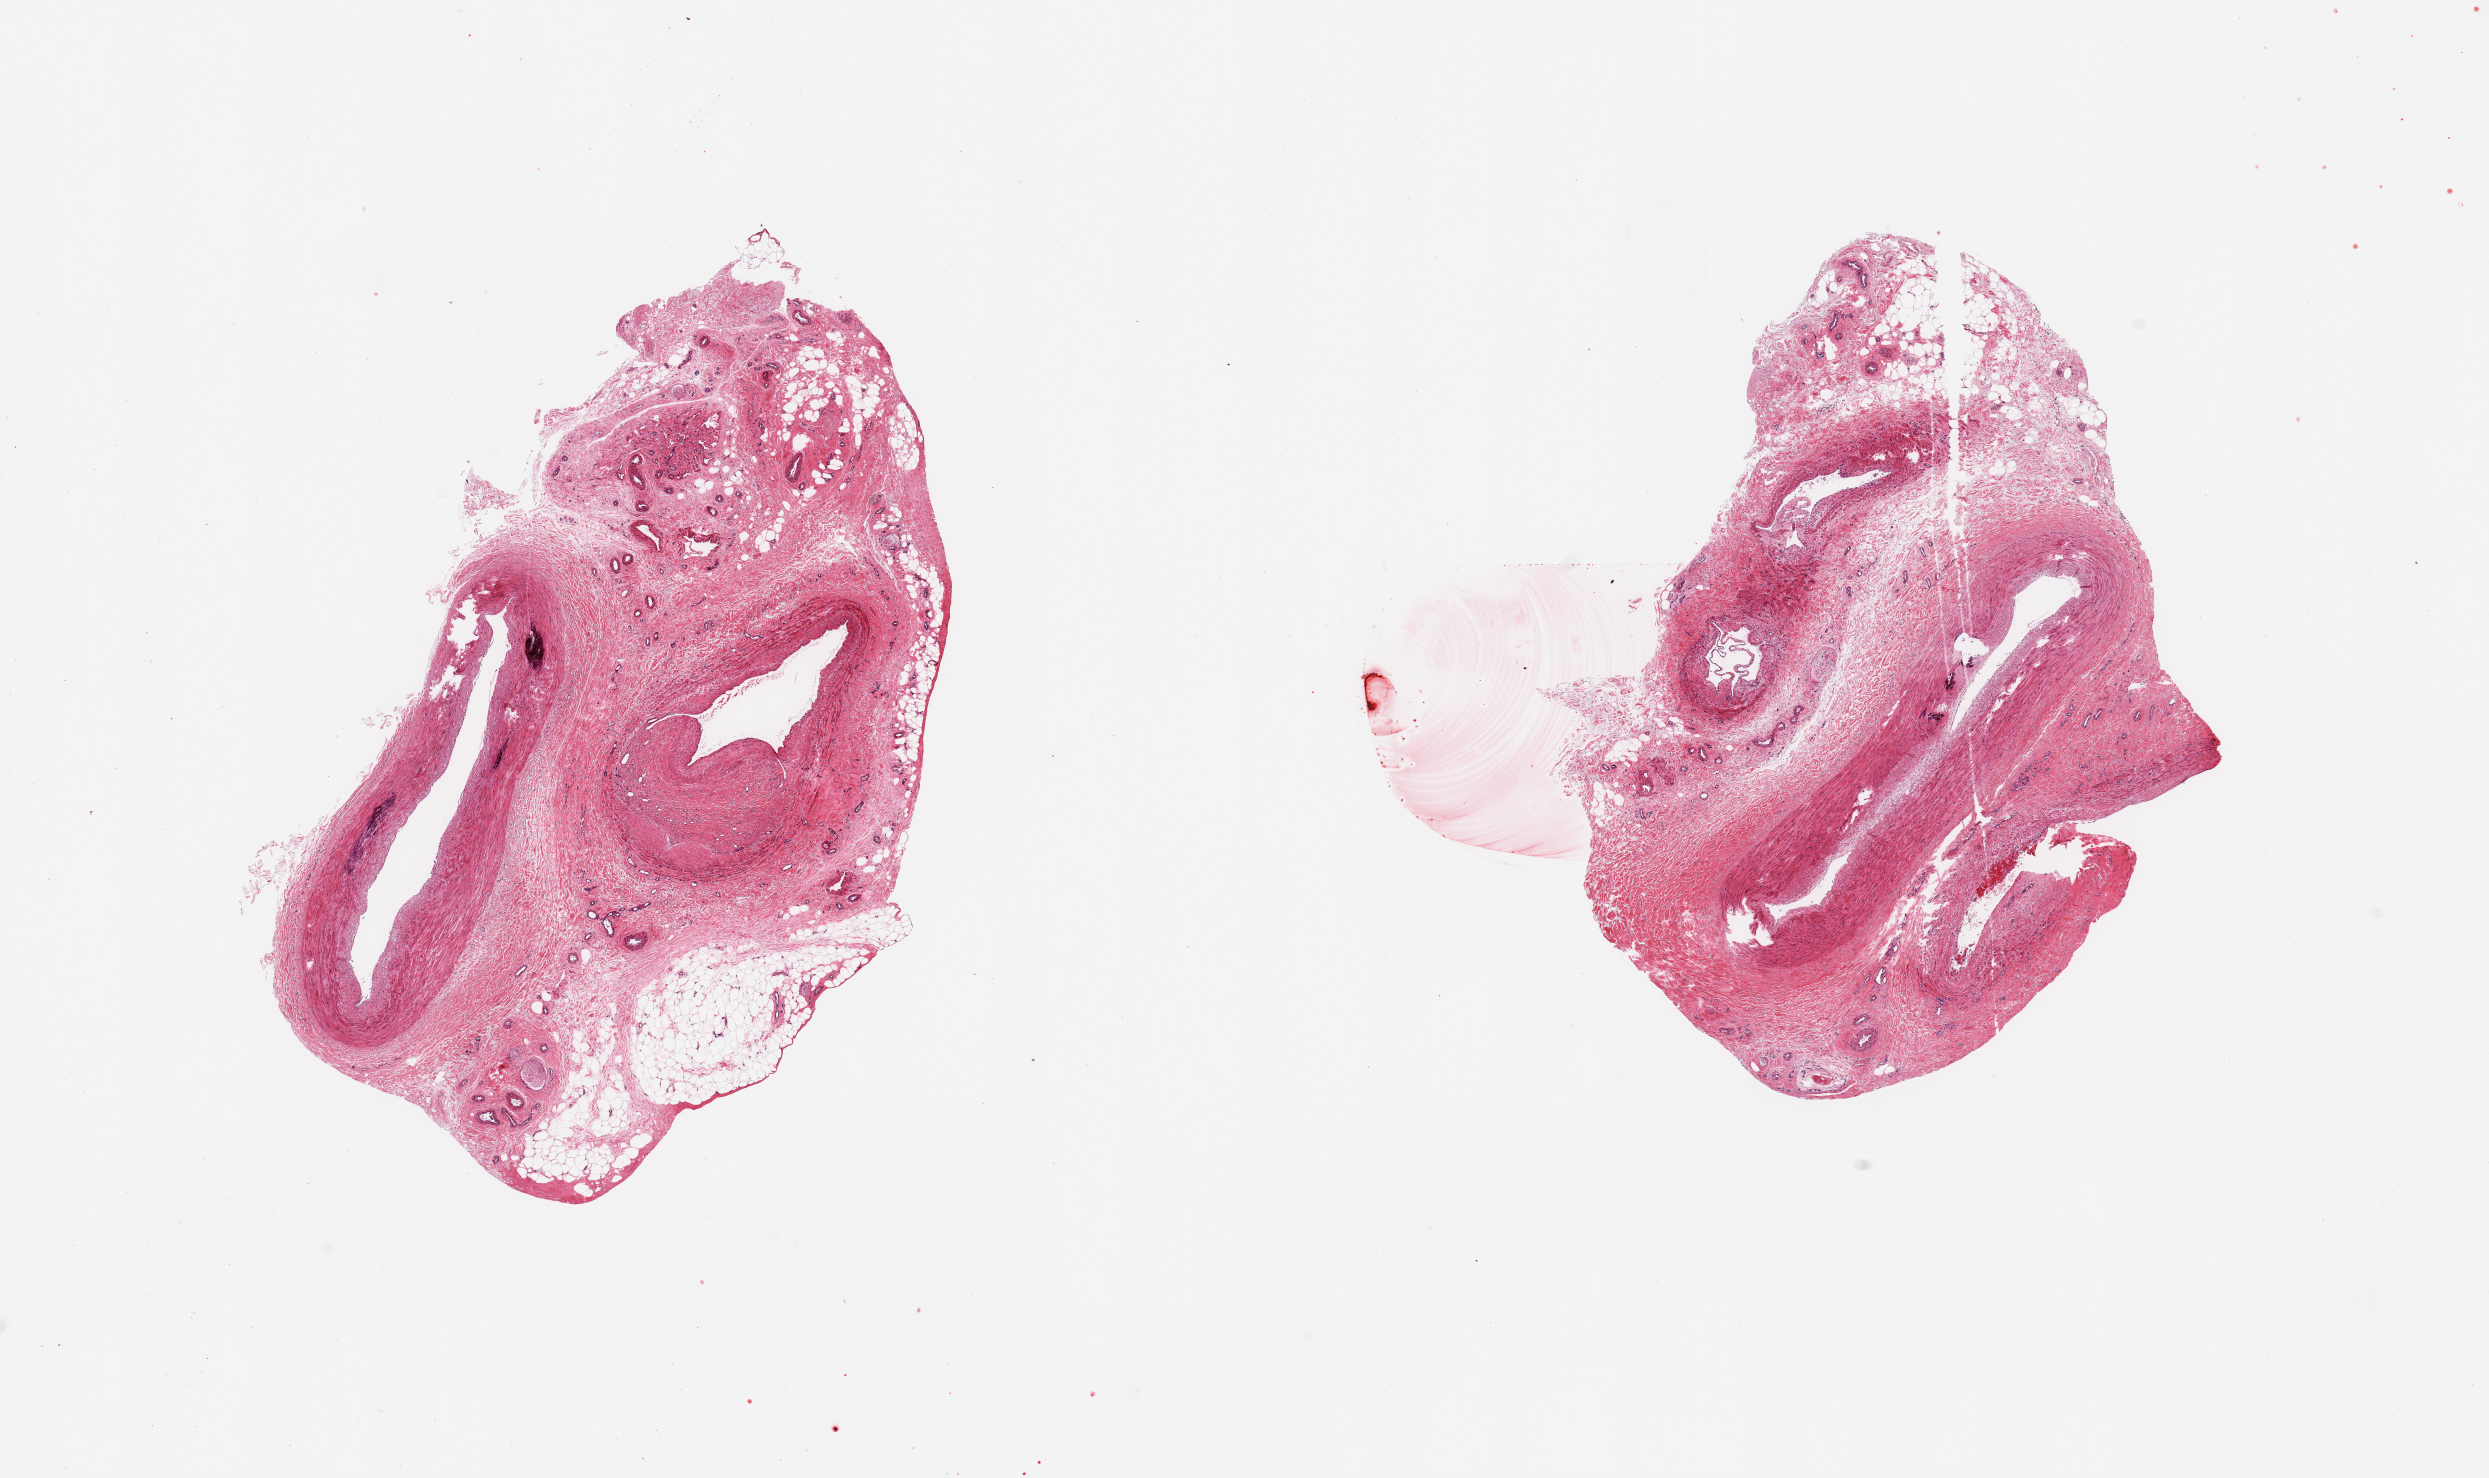
Hematoxylin and eosin (H&E) whole-slide image, a low-resolution overview of the entire scanned area, about 19.7 x 11.7 mm (acquisition: 20x scan), PAXgene-fixed paraffin-embedded (PFPE) section, section of tibial artery (target tissue), tissue donor sample. Donor: female.
* reviewer comment on this tissue sample: 2 pieces; medial calcific sclerosis, both include significant extraneous tissue (fat, vein)